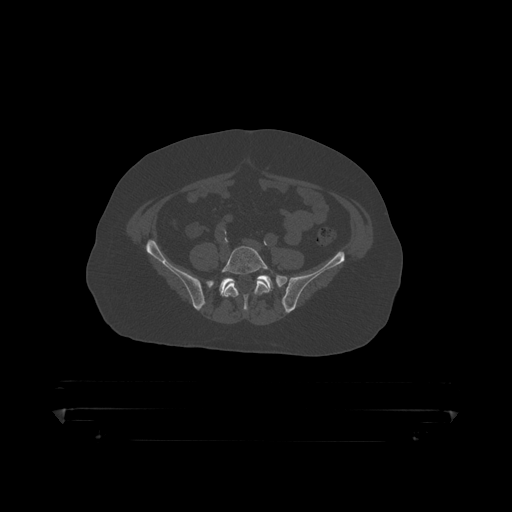
CT including the spine, one axial slice; position 35 of 390 along the scan axis; reconstruction kernel STANDARD; 120 kVp; bone window (W 1800 / L 400 HU); 1.25 mm slice thickness; 512 × 512 image matrix. Patient: male, 60 years. Case-level facts recorded for this patient, not image findings: primary cancer: prostate.
Annotated regions visible in this slice (semi-automatically segmented with operator editing):
- L5 vertebra: box from (x=221, y=246) to (x=275, y=313) px